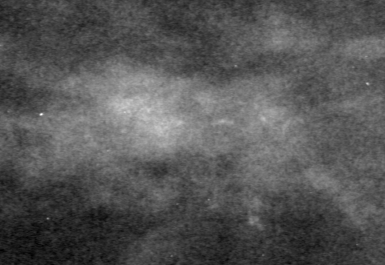
Cropped region of a digitized screen-film mammogram centred on a radiologist-marked abnormality; left breast; CC view; BI-RADS breast density category 2 (scale 1–4).
Marked abnormality: calcifications, morphology pleomorphic, distribution clustered; BI-RADS assessment category 4; subtlety rating 1 on a 1 (subtle) to 5 (obvious) scale; pathology (as recorded): malignant.